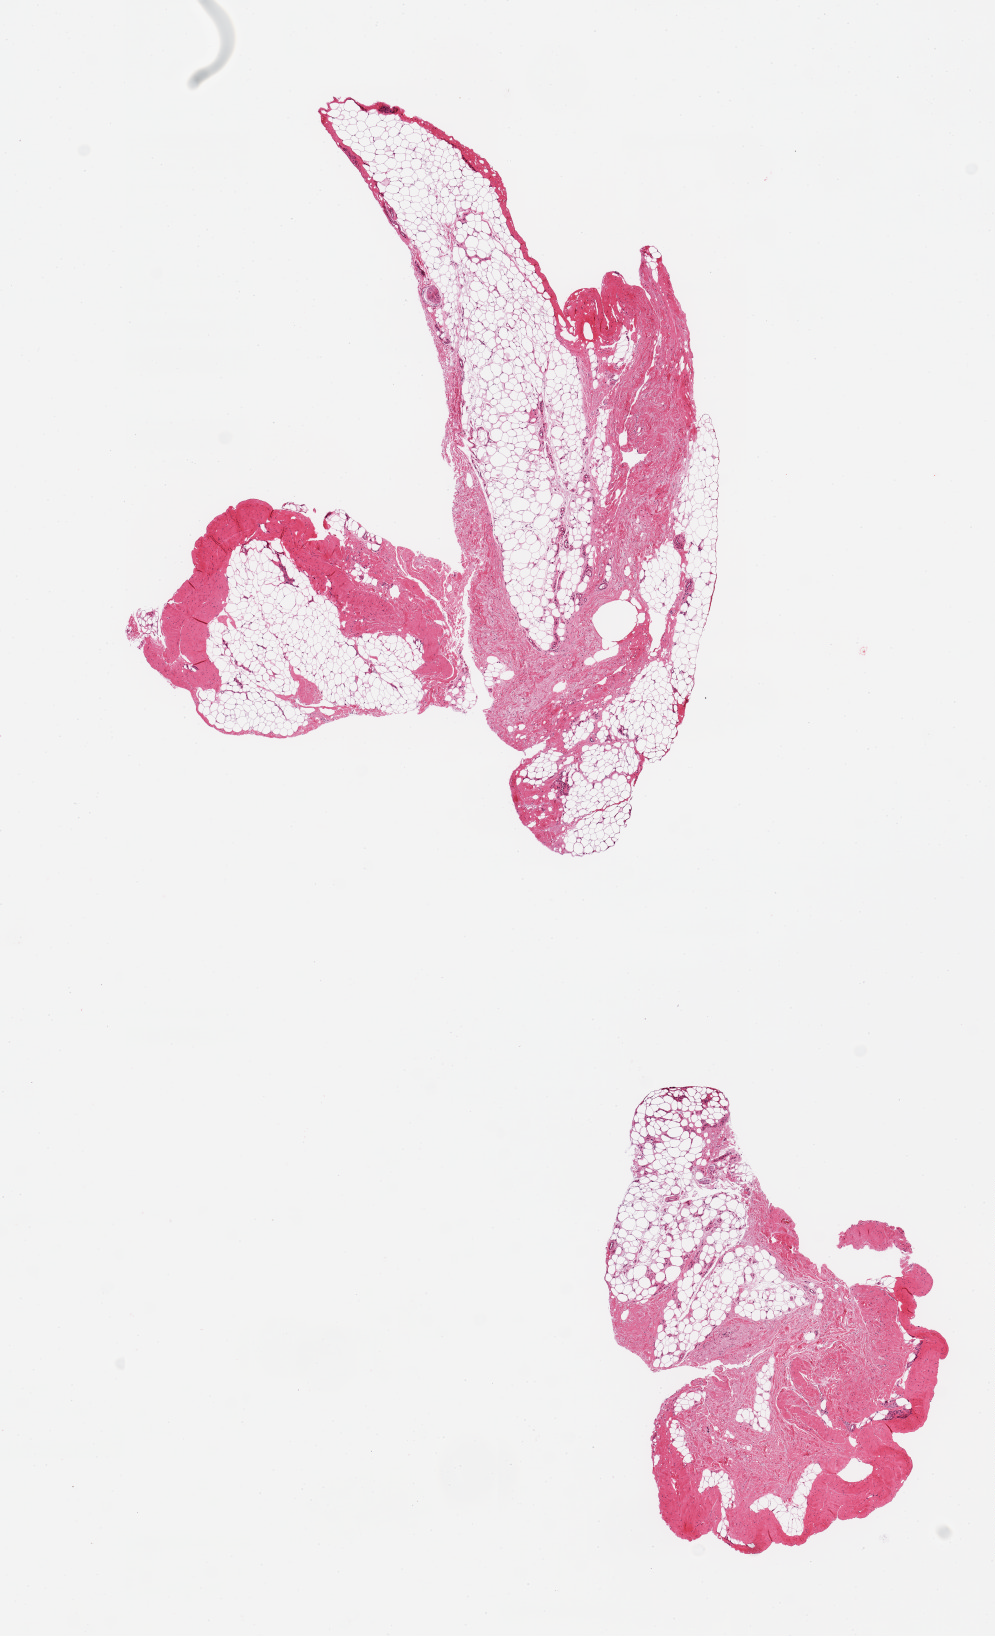
Digitized hematoxylin and eosin (H&E)-stained section, whole scanned area (about 7.9 x 12.9 mm) shown as a low-resolution overview. PAXgene-fixed, paraffin-embedded tissue. Sampled site (target tissue): tibial nerve. Tissue donor sample. Donor: female.
- reviewer comment on this tissue sample: 2 pieces, adipose tissue, collagenized fibroconnective tissue, no peripheral nerve elements